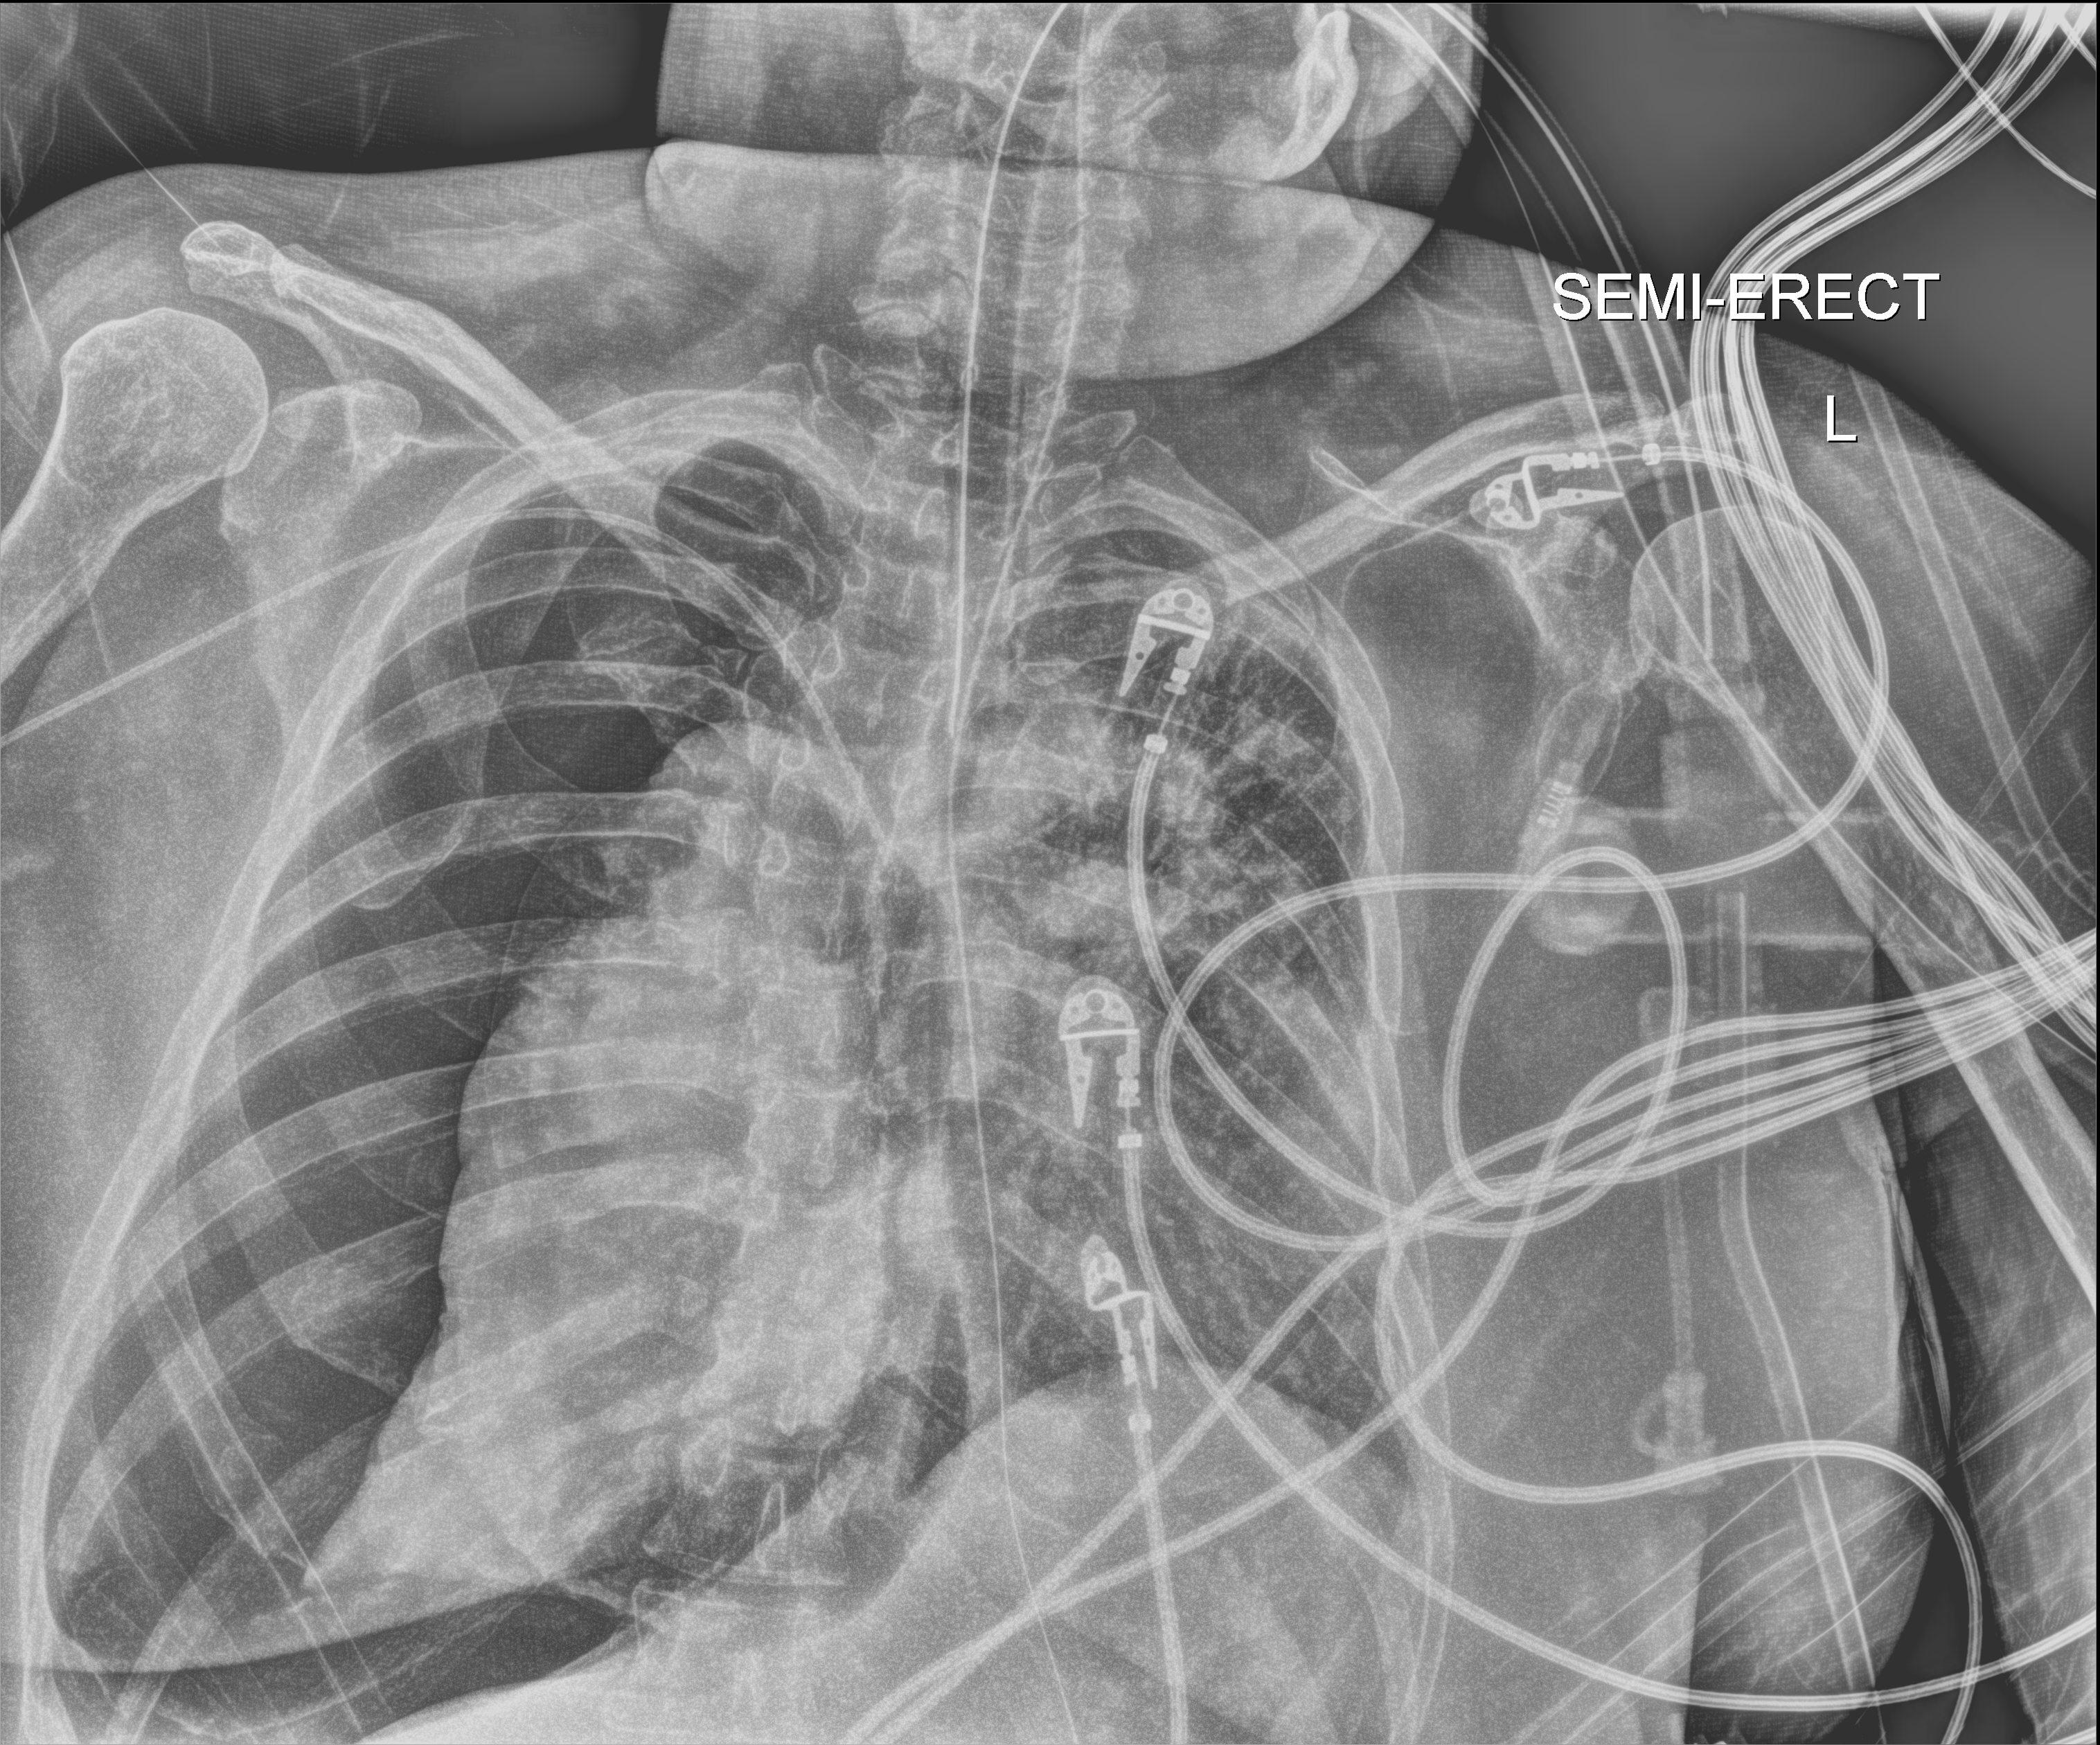
Bedside chest radiograph (digital radiography); anteroposterior (AP) projection. Adult patient hospitalised with COVID-19, age 18–59 years.
Admission-level facts for this patient (not findings on this image; timing relative to this image not recorded): mechanically ventilated during this hospital stay: yes; admitted to intensive care during this hospital stay: yes.